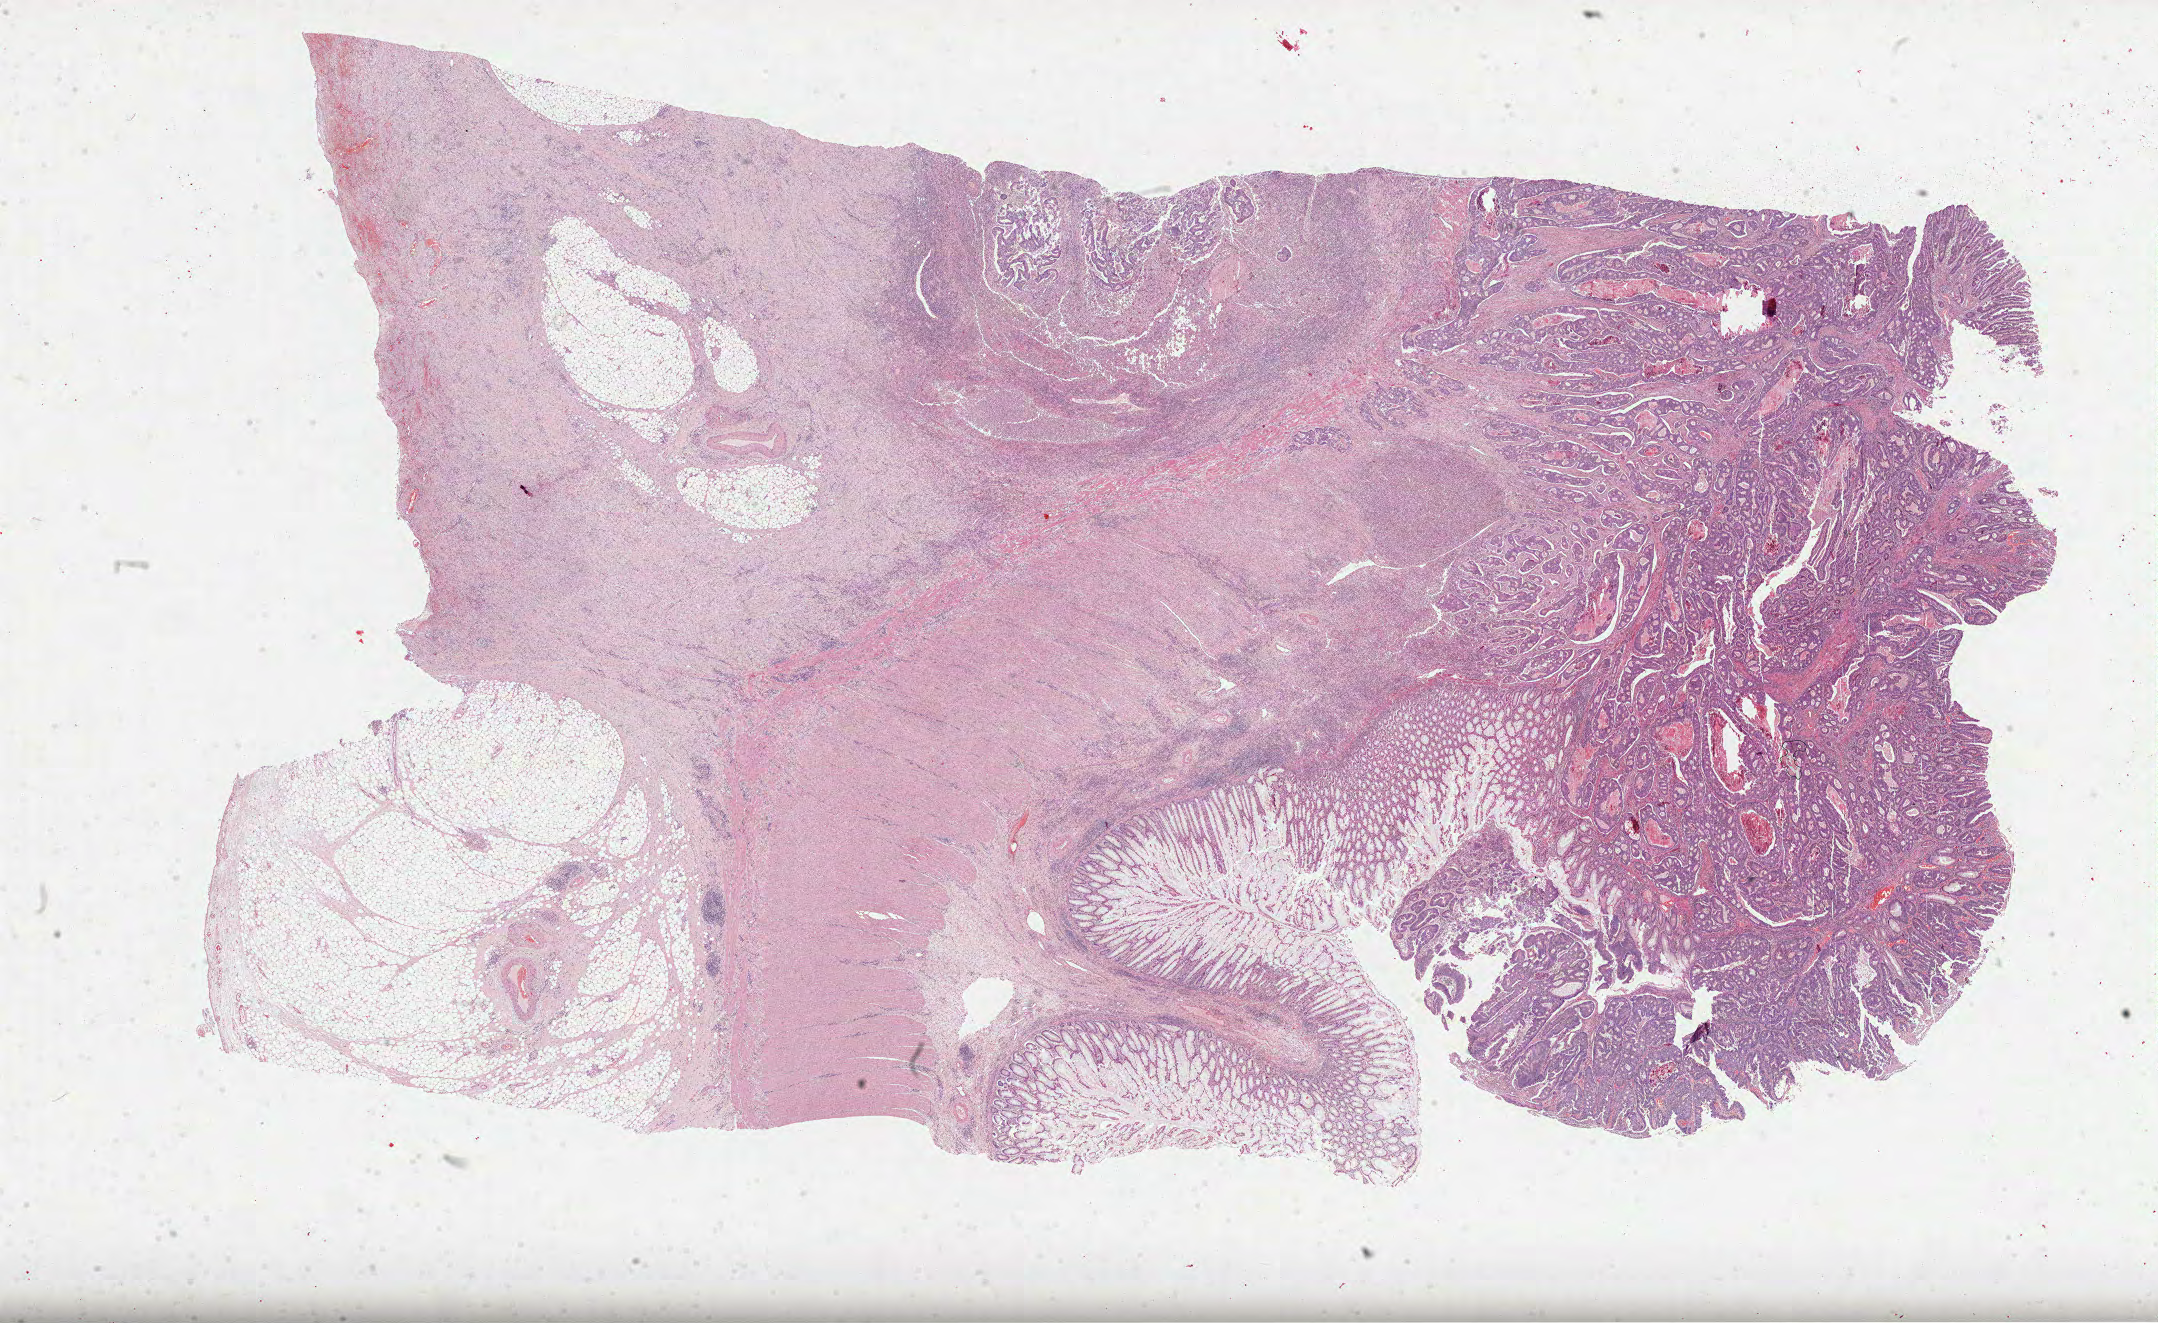
Whole-slide histology image, Hematoxylin and eosin (H&E) stained — low-resolution overview of the scanned area, about 34.8 x 21.3 mm (from a 40x scan); FFPE section; primary tumour sample from the colon. Female, age 49 years at initial diagnosis.
AJCC pathologic stage: IV (7th edition). Lymph nodes positive (case pathology): 1 of 12 examined. Histologic diagnosis: Adenocarcinoma, NOS.